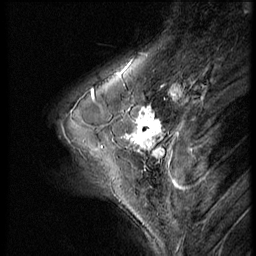
Breast MRI (dynamic contrast-enhanced), one sagittal slice; position 17 of 56 along the scan axis; dynamic contrast-enhanced series, image 2 of 3 at this slice position (ordered by acquisition); 1.5 T; TE 4.2 ms, TR 9 ms; 2.5 mm slice thickness; 256 × 256 image matrix, field of view 180 × 180 mm. Female patient, age 46 years. From the clinical record (not read from this slice): setting: breast cancer imaged before/during neoadjuvant chemotherapy; receptor status: HER2-positive.
Structures marked on this image (semi-automatic segmentation, software-assisted and operator-edited):
- analysis volume of interest (the breast-tissue region the enhancement analysis was run in; not a lesion): bounding box <64,98,174,182> (left, top, right, bottom; pixels)
- tumour enhancement mask (voxels above the 140 % enhancement threshold inside the analysis volume of interest): <127,108,163,154>